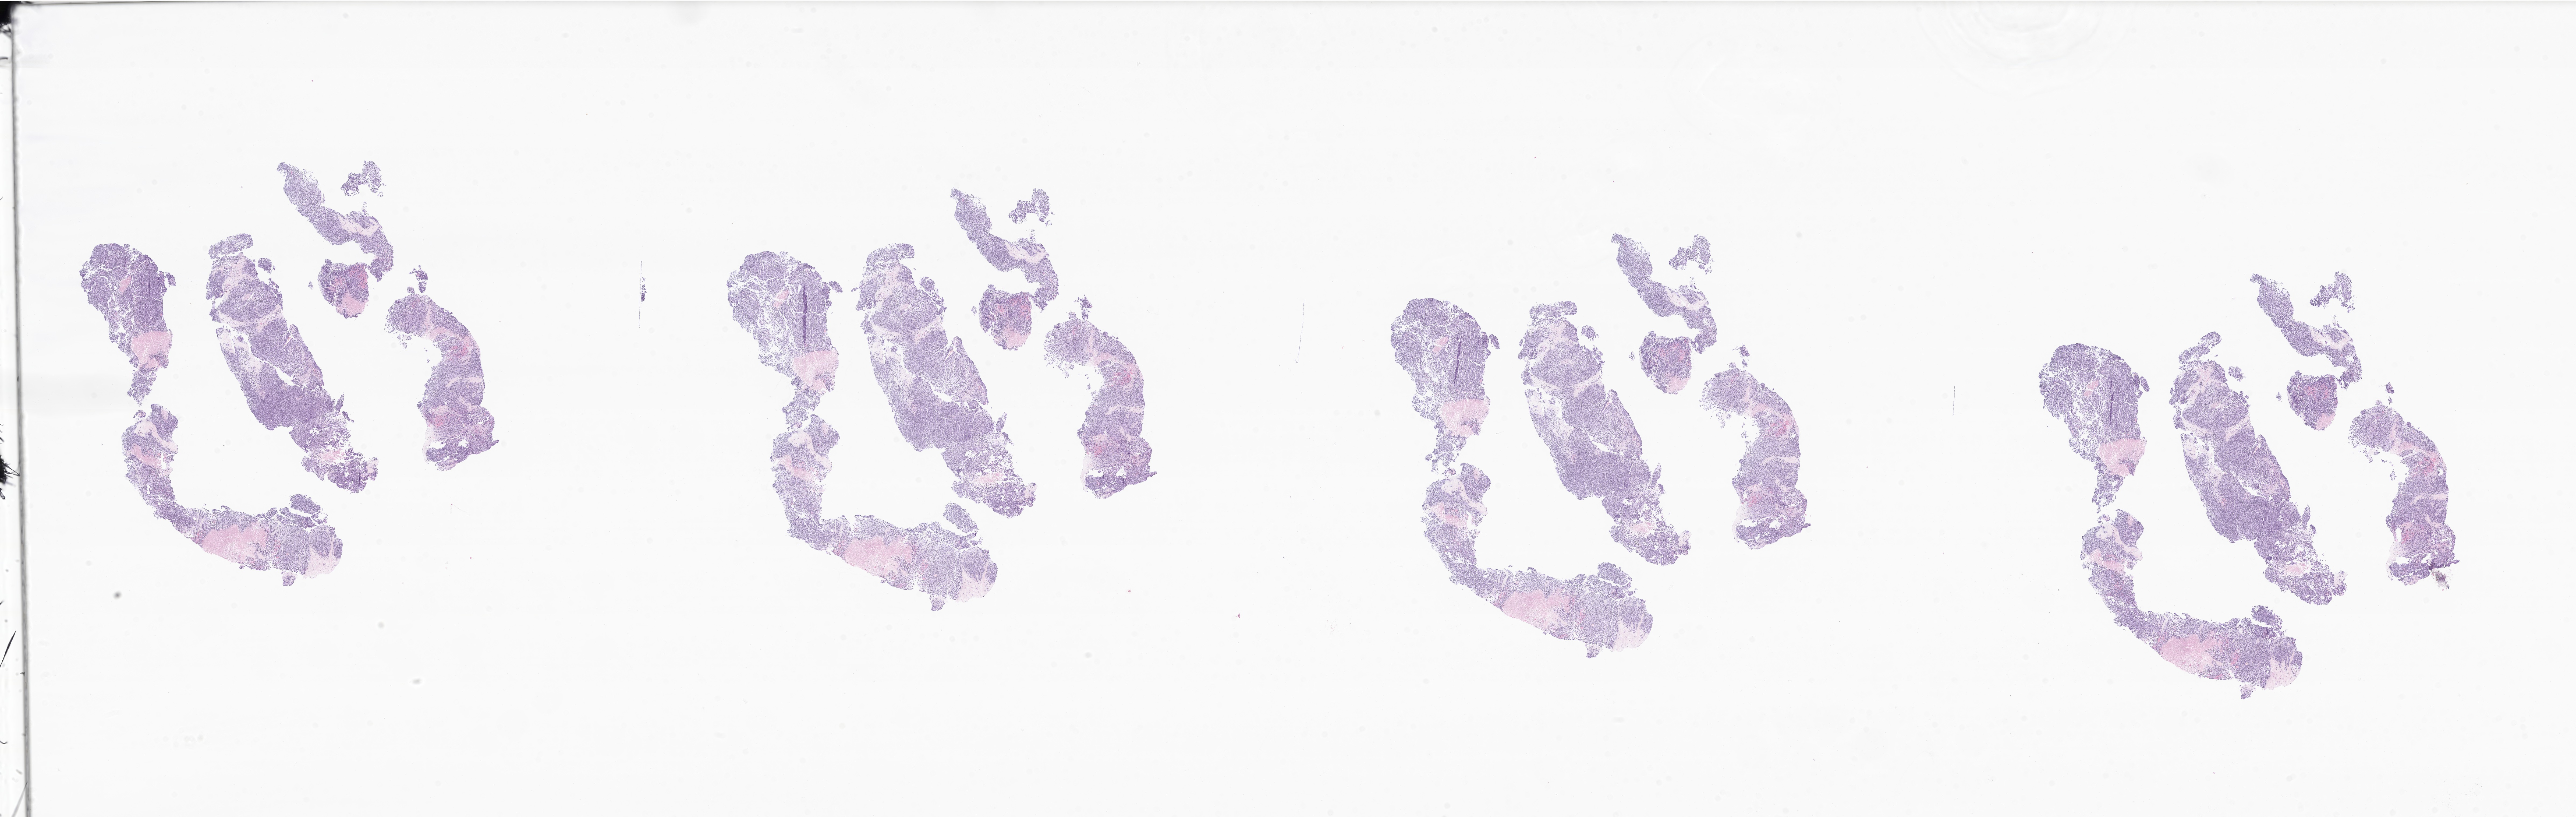
H&E whole-slide image of tumor tissue from the pleura — low-resolution overview of the scanned area, about 40.4 x 12.8 mm; formalin-fixed, paraffin-embedded (FFPE) tissue. Patient female; age 206 months (17 years 2 months).
• diagnosis: Alveolar rhabdomyosarcoma